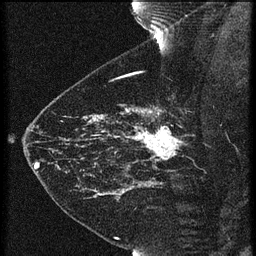
Breast MRI (dynamic contrast-enhanced), one sagittal slice; position 47 of 60 along the scan axis; 3 images stored at this slice position (order not interpretable as contrast timing); 1.5 T; TE 4.2 ms, TR 21.3 ms; 1.5 mm slice thickness; 256 × 256 image matrix, field of view 180 × 180 mm. Patient: female, 43 years. From the clinical record (not read from this slice): setting: breast cancer imaged before/during neoadjuvant chemotherapy; receptor status: HER2-positive.
Annotated regions visible in this slice (semi-automatically segmented with operator editing):
- analysis volume of interest (the breast-tissue region the enhancement analysis was run in; not a lesion): bounding box <119,114,189,173> (left, top, right, bottom; pixels)
- tumour enhancement mask (voxels above the 90 % enhancement threshold inside the analysis volume of interest): <129,114,183,161>